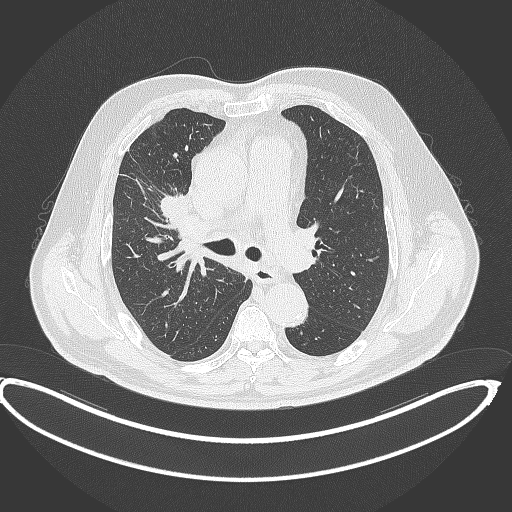
Chest CT, one axial slice. Slice 259 of 390 in the series (ordered by position). Reconstruction kernel B70f. 120 kVp. Lung window (W 1500 / L -600 HU). 512 × 512 image matrix, field of view 448 × 448 mm. Patient: male, 62 years. Case-level facts recorded for this patient, not image findings: clinical TNM (as recorded): T1c N3 M1c.
Annotated regions visible in this slice (rectangle marked by the reading radiologist):
- lung tumour (recorded histology: adenocarcinoma): bounding box [x1, y1, x2, y2] px = [154, 190, 190, 219]